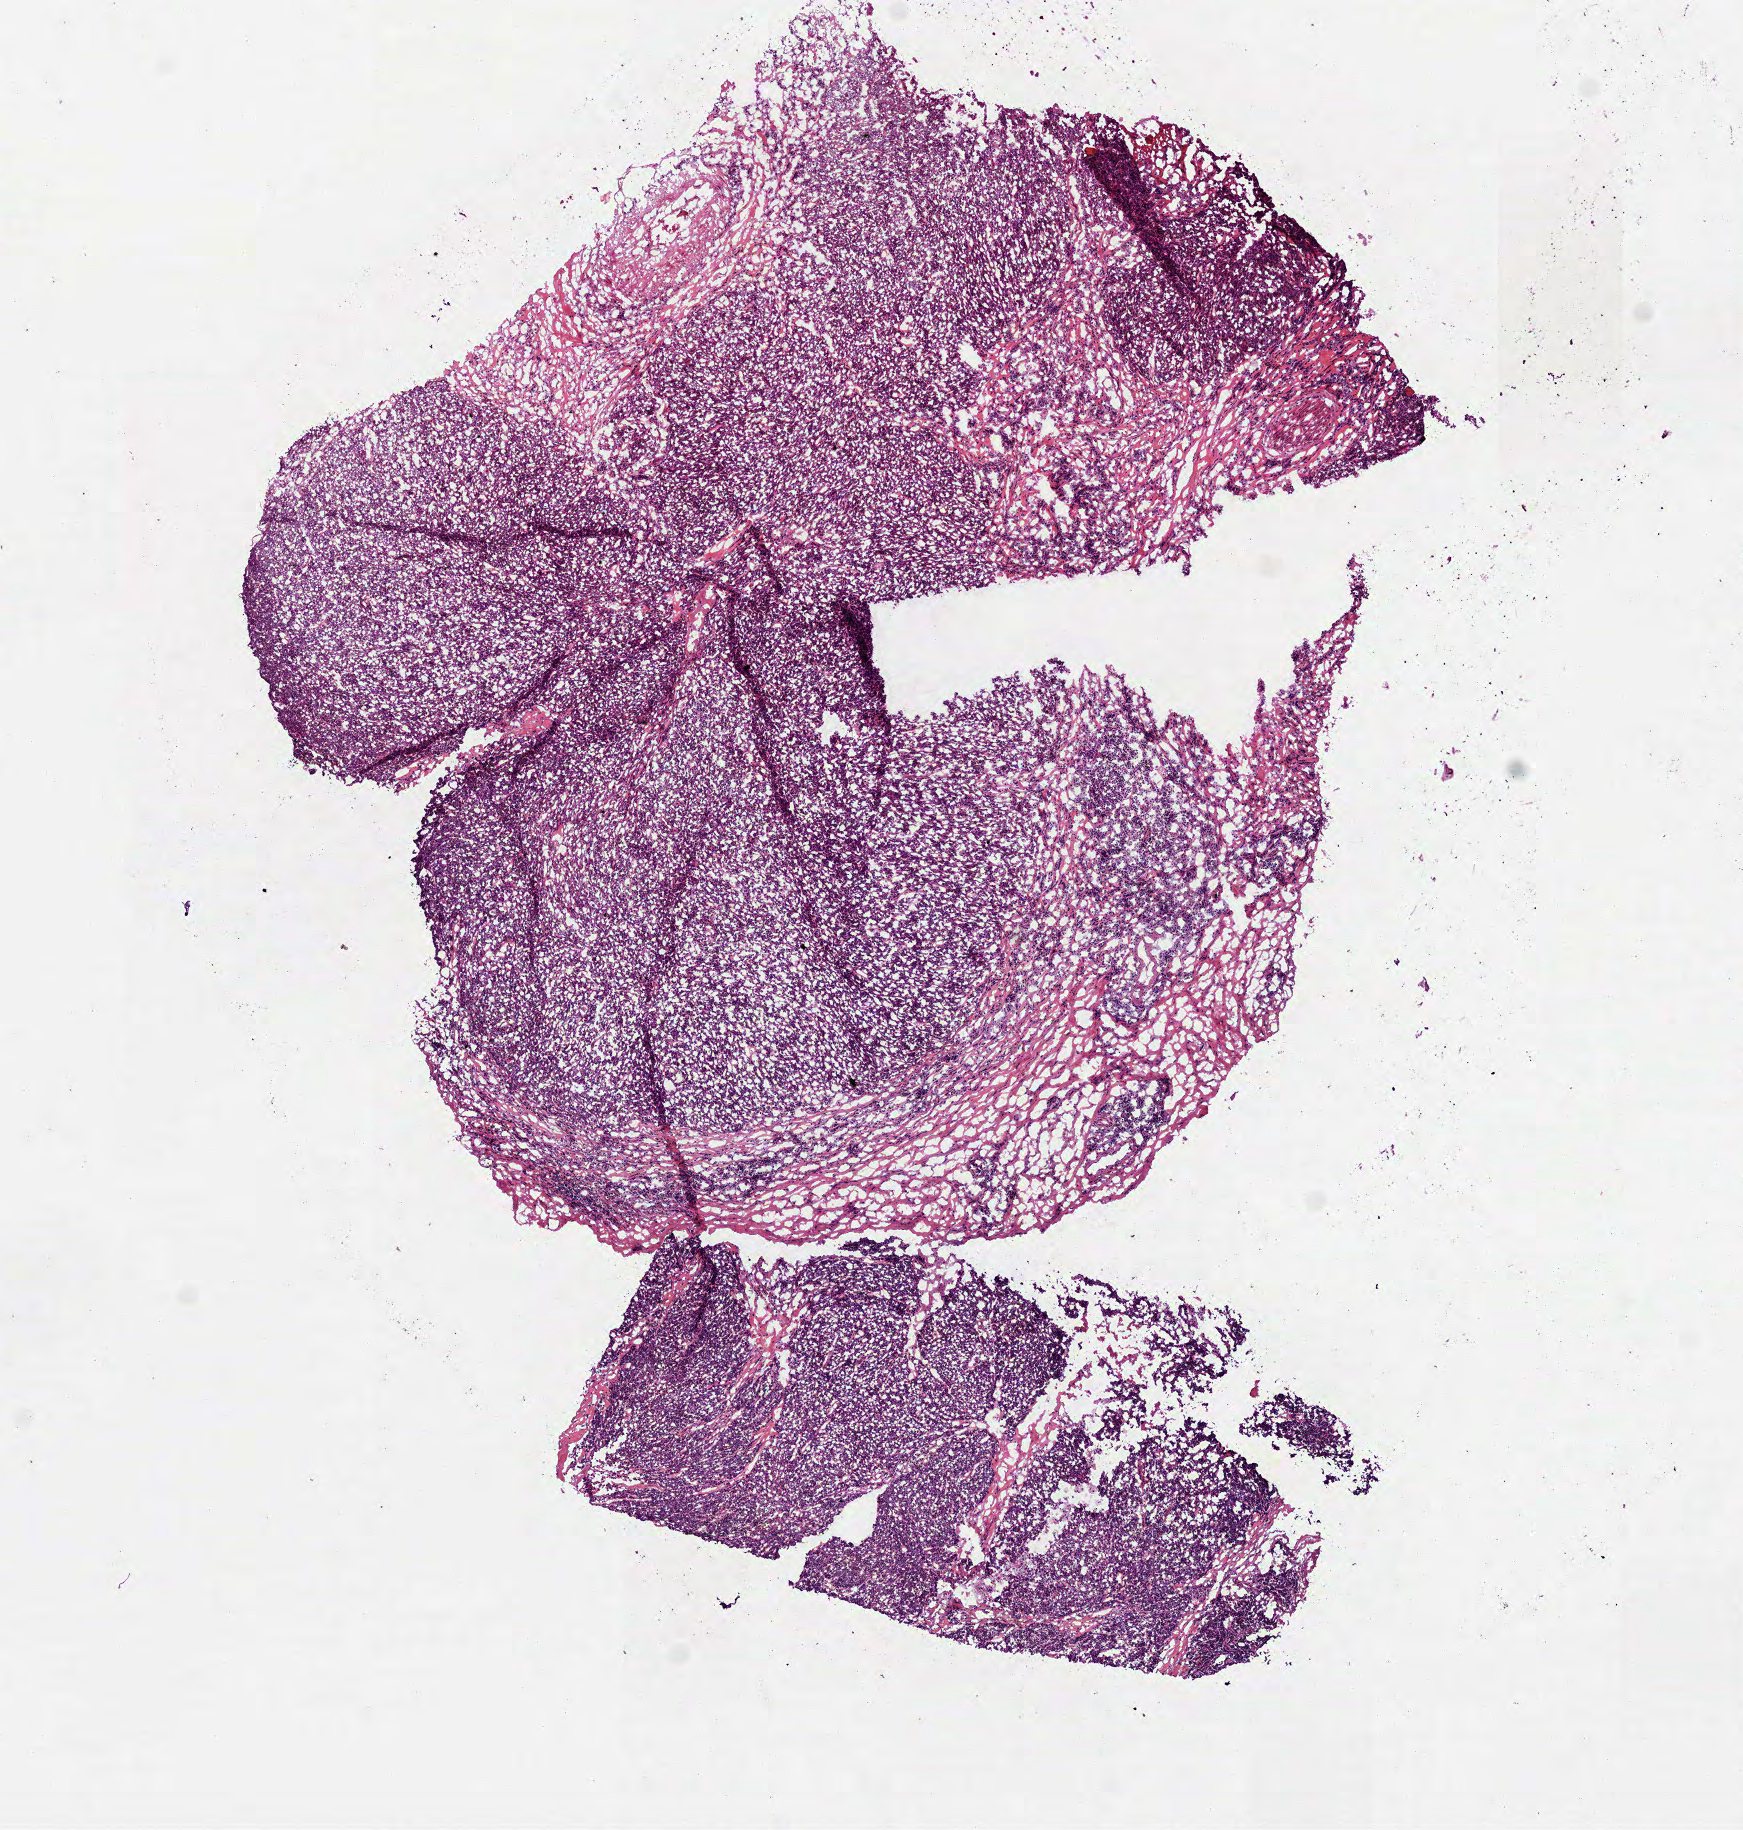
H&E whole-slide image, whole scanned area (about 7.0 x 7.4 mm, slide scanned at 40x) shown as a low-resolution overview, frozen section from the bottom of the tissue portion, sample: primary tumour, head and neck. Patient: male, age at initial diagnosis 57 years. Histologic grade: G3 (poorly differentiated). Pathologist review of this section (percent, as recorded): tumour cells 80%, tumour nuclei 70%, normal cells 0%, stromal cells 20%, necrosis 0%. Infiltration values recorded for this section: lymphocyte infiltration 25%, monocyte infiltration 0%, neutrophil infiltration 0%.
• diagnosis: Squamous cell carcinoma, NOS (tongue, NOS)
• AJCC pathologic stage: II
• TNM: T2 N0